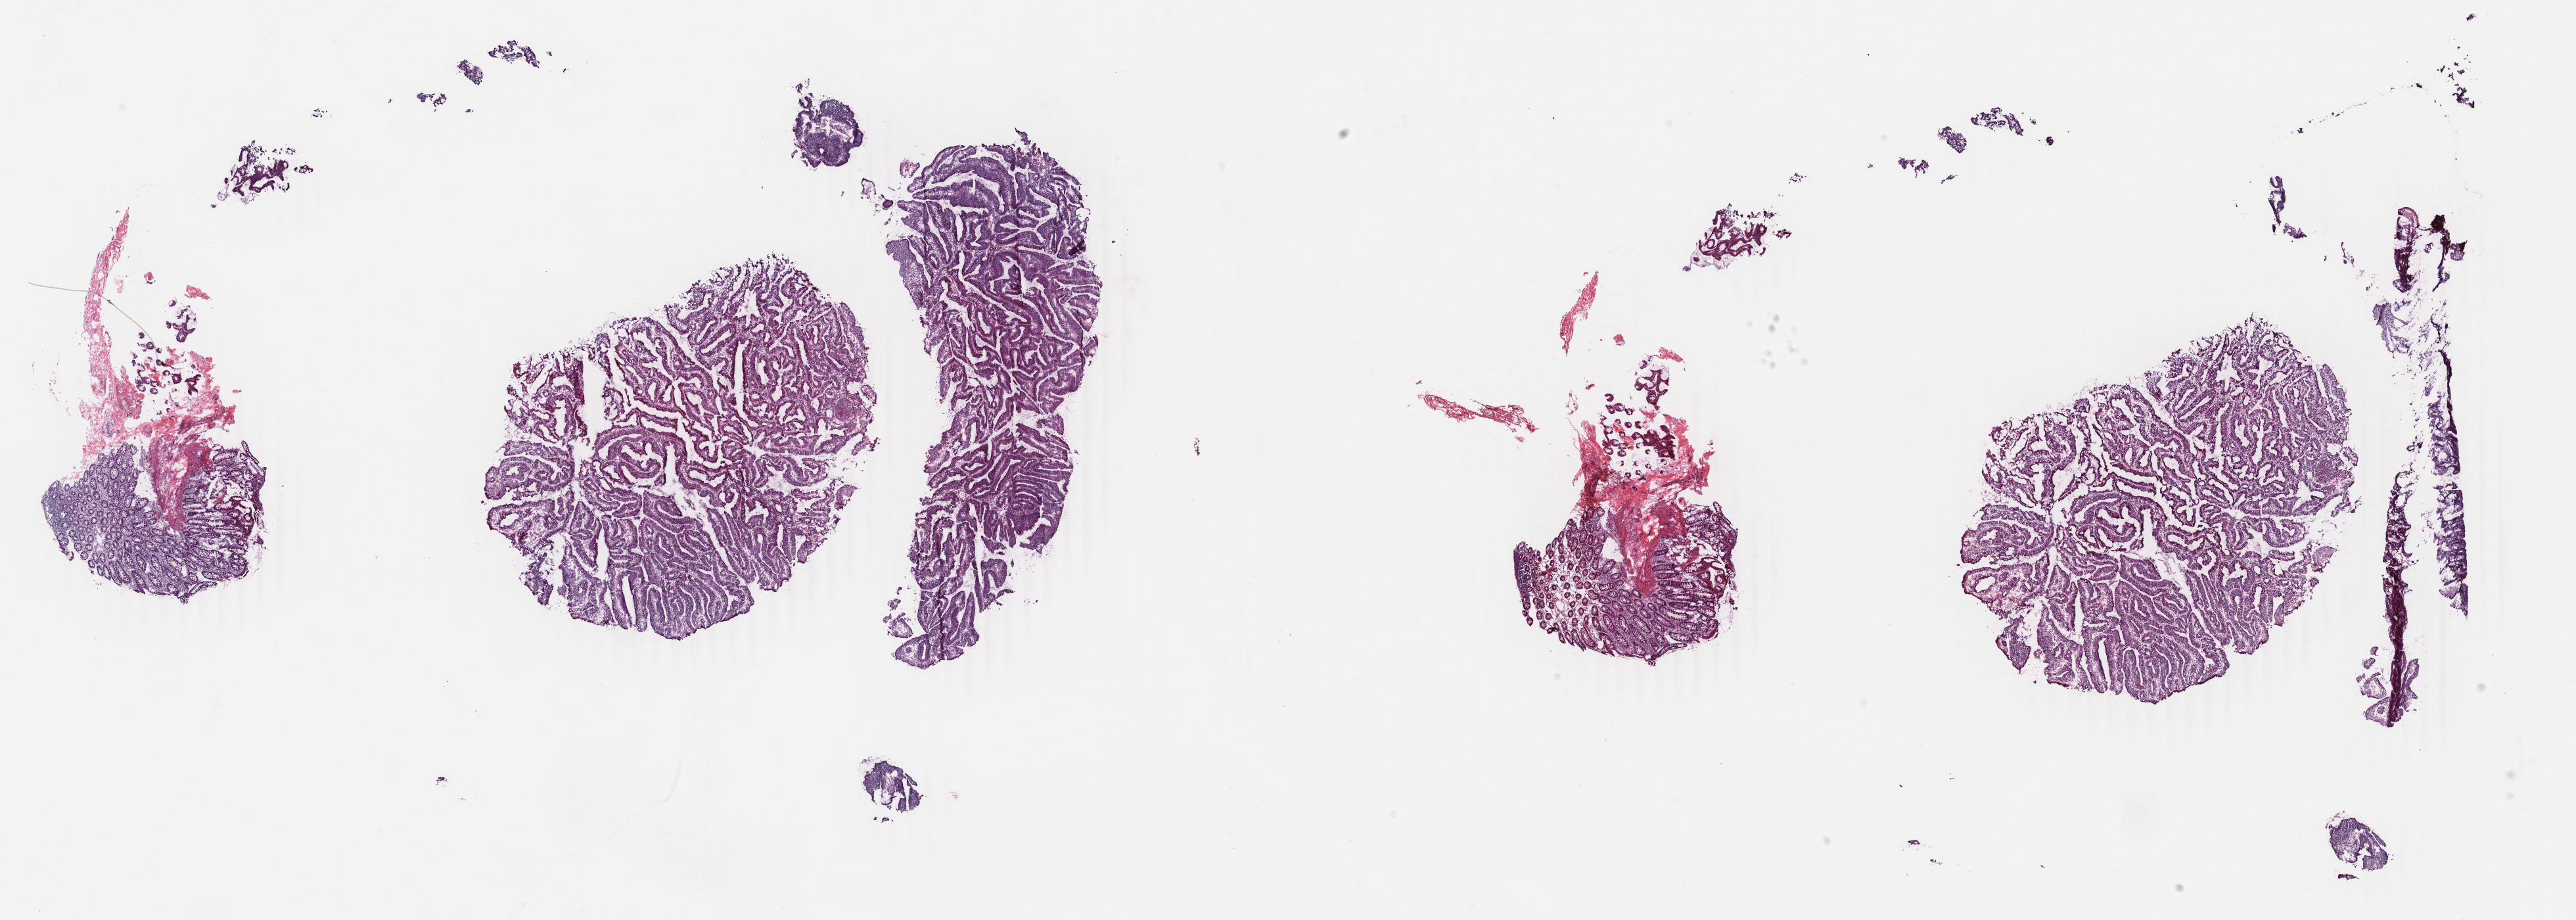
H&E whole-slide image — a low-resolution overview of the entire scanned area, about 31.2 x 11.1 mm (acquisition: 40x scan), frozen section, colon, primary tumour sample. Male patient; age at initial diagnosis 73 years. Pathologist review of this section (percent, as recorded): tumour cells 64%, tumour nuclei 70%, normal cells 25%, stromal cells 10%, necrosis 1%. Inflammatory infiltration, as recorded: lymphocyte infiltration 10%, monocyte infiltration 1%, neutrophil infiltration 1%.
- lymph nodes positive (case pathology): 0 of 18 examined
- TNM: T2 N0 M0
- pathologic diagnosis: Adenocarcinoma, NOS
- AJCC pathologic stage: I (6th edition)